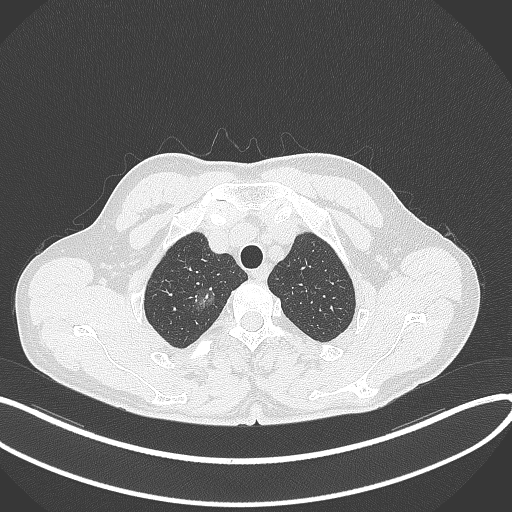
Chest CT, one axial slice; position 329 of 407 along the scan axis; reconstruction kernel B70f; lung window (W 1500 / L -600 HU); 1 mm slice thickness; 512 × 512 image matrix, field of view 400 × 400 mm. Patient: male, 58 years. Case-level facts recorded for this patient, not image findings: clinical TNM (as recorded): T1c N0 M0; histopathological grade: G1-2.
Structures marked on this image (rectangle marked by the reading radiologist):
- lung tumour (recorded histology: adenocarcinoma): bounding box [x1, y1, x2, y2] px = [192, 284, 224, 318]